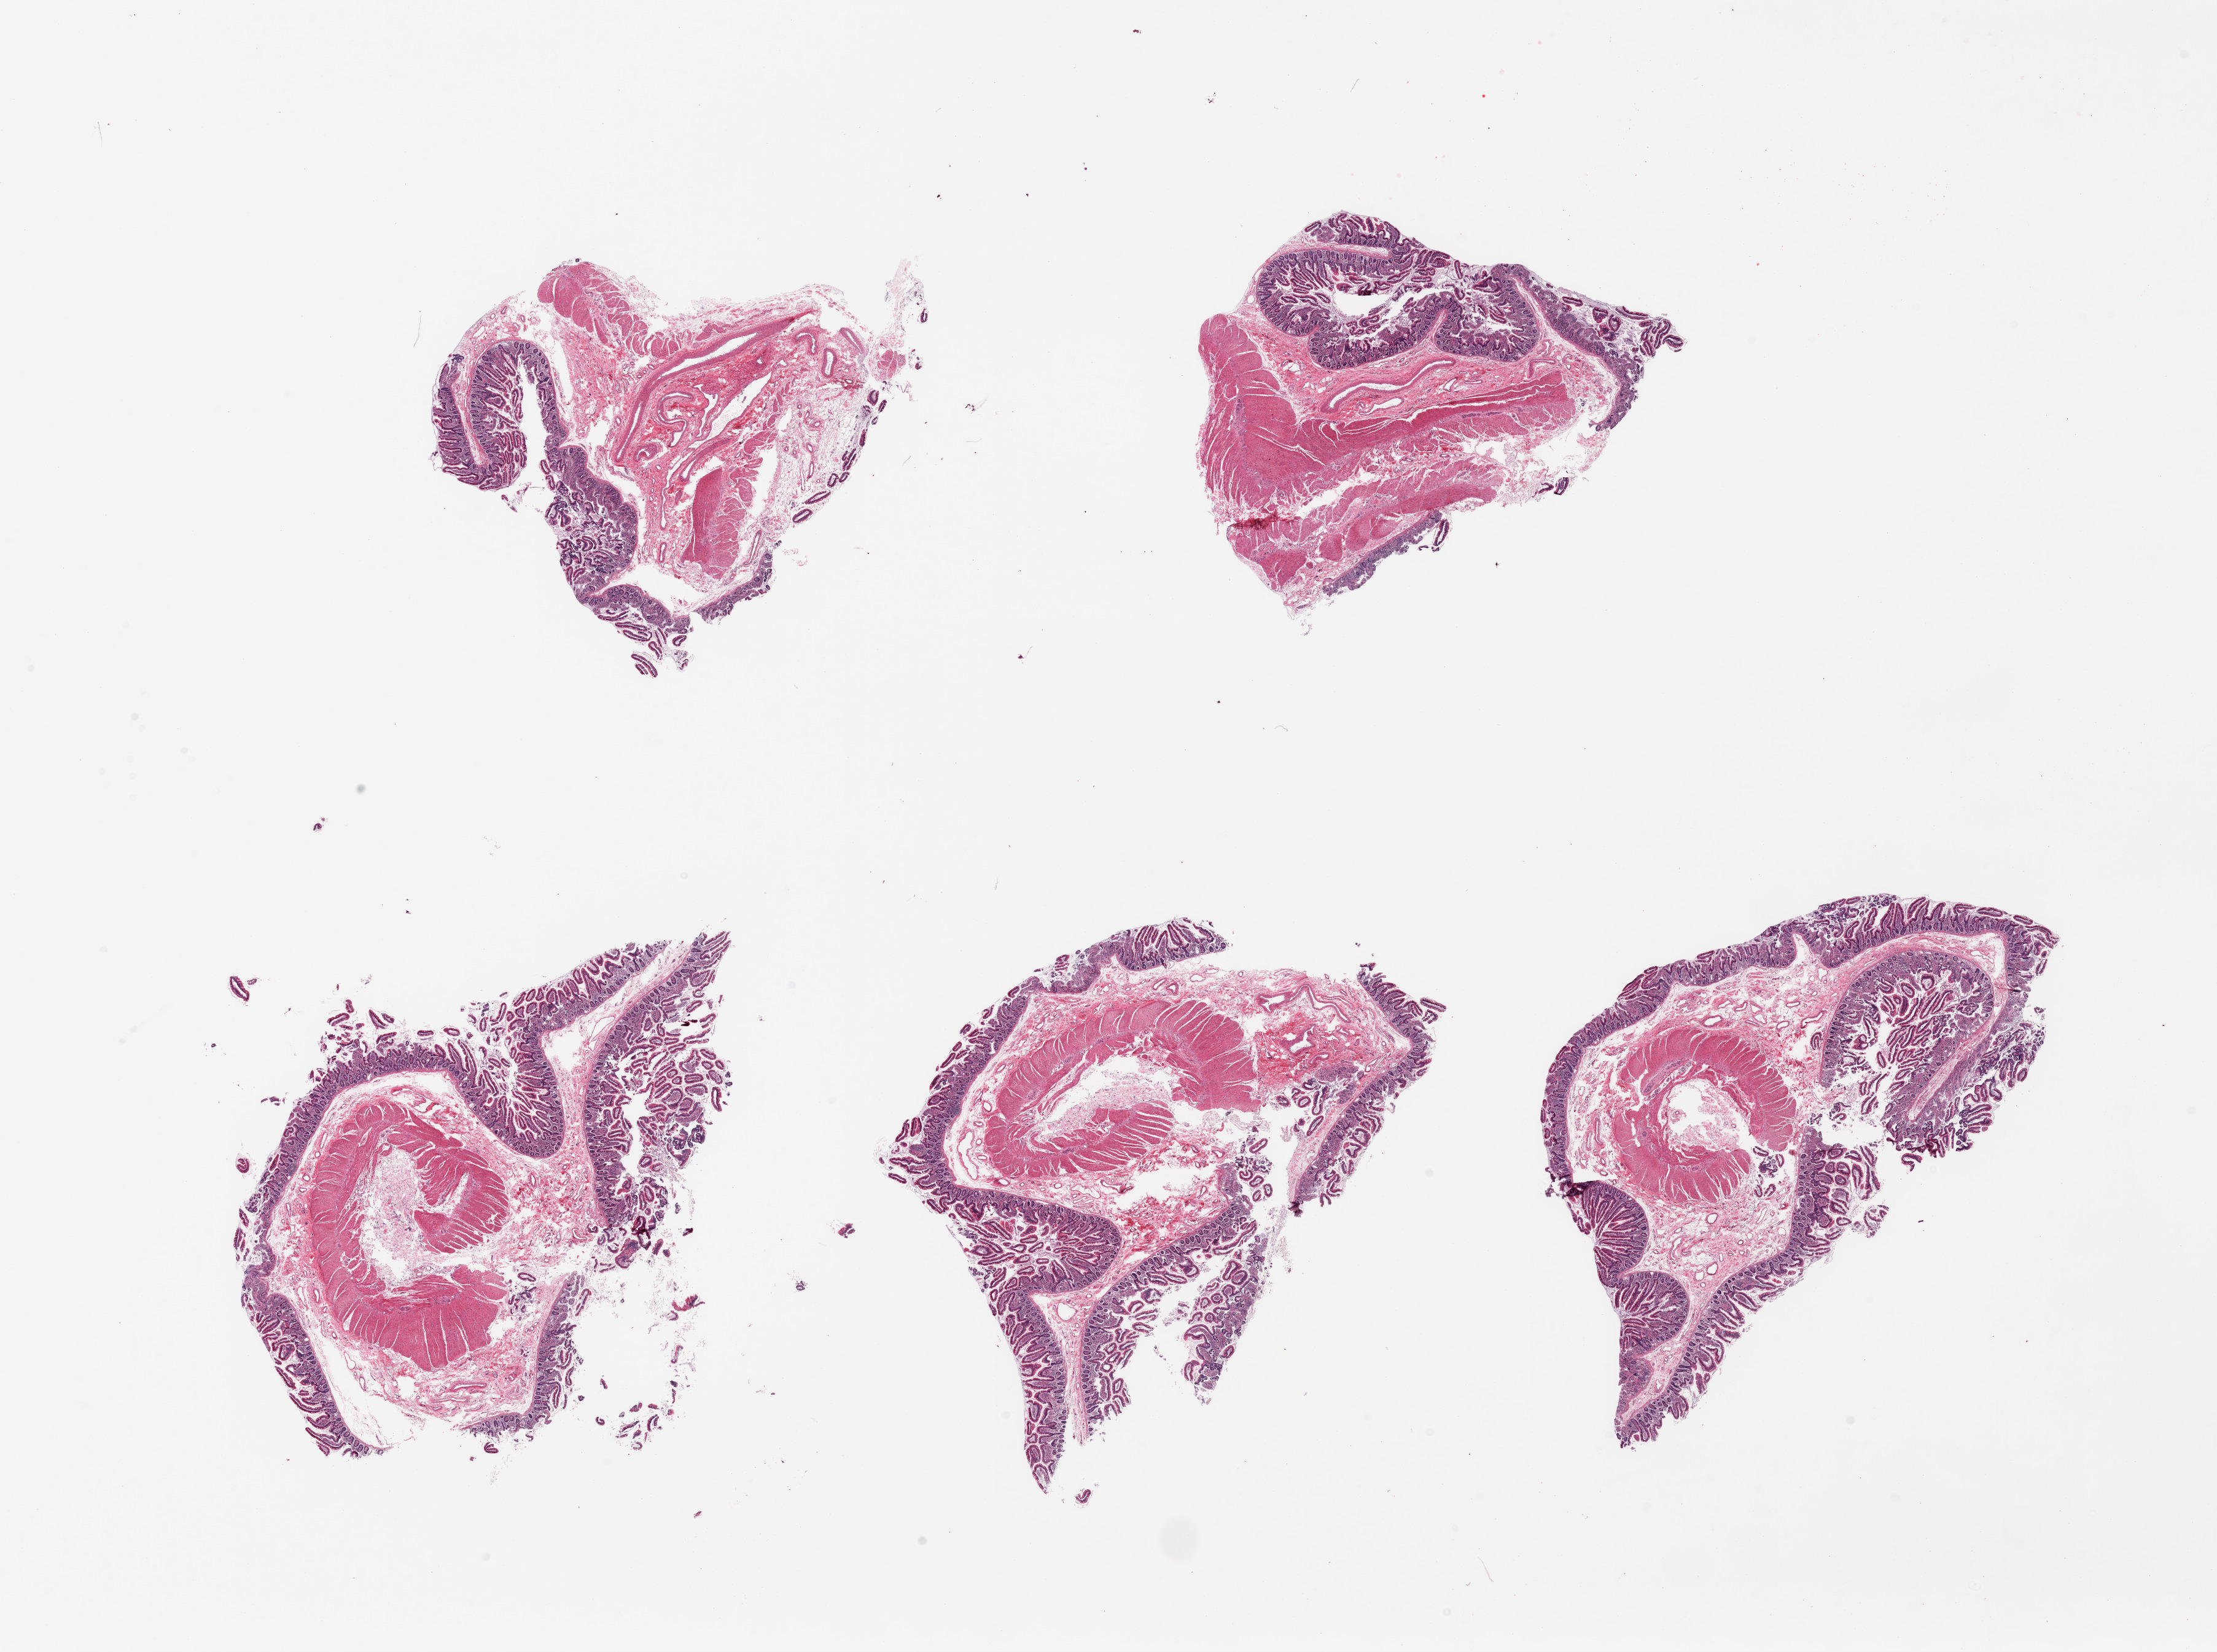
Digitized H&E-stained section — low-resolution overview of the scanned area, about 28.5 x 21.3 mm (acquisition: 20x scan). Male donor.
Specimen: PAXgene-fixed paraffin-embedded (PFPE) section; target tissue: transverse colon; tissue donor sample.